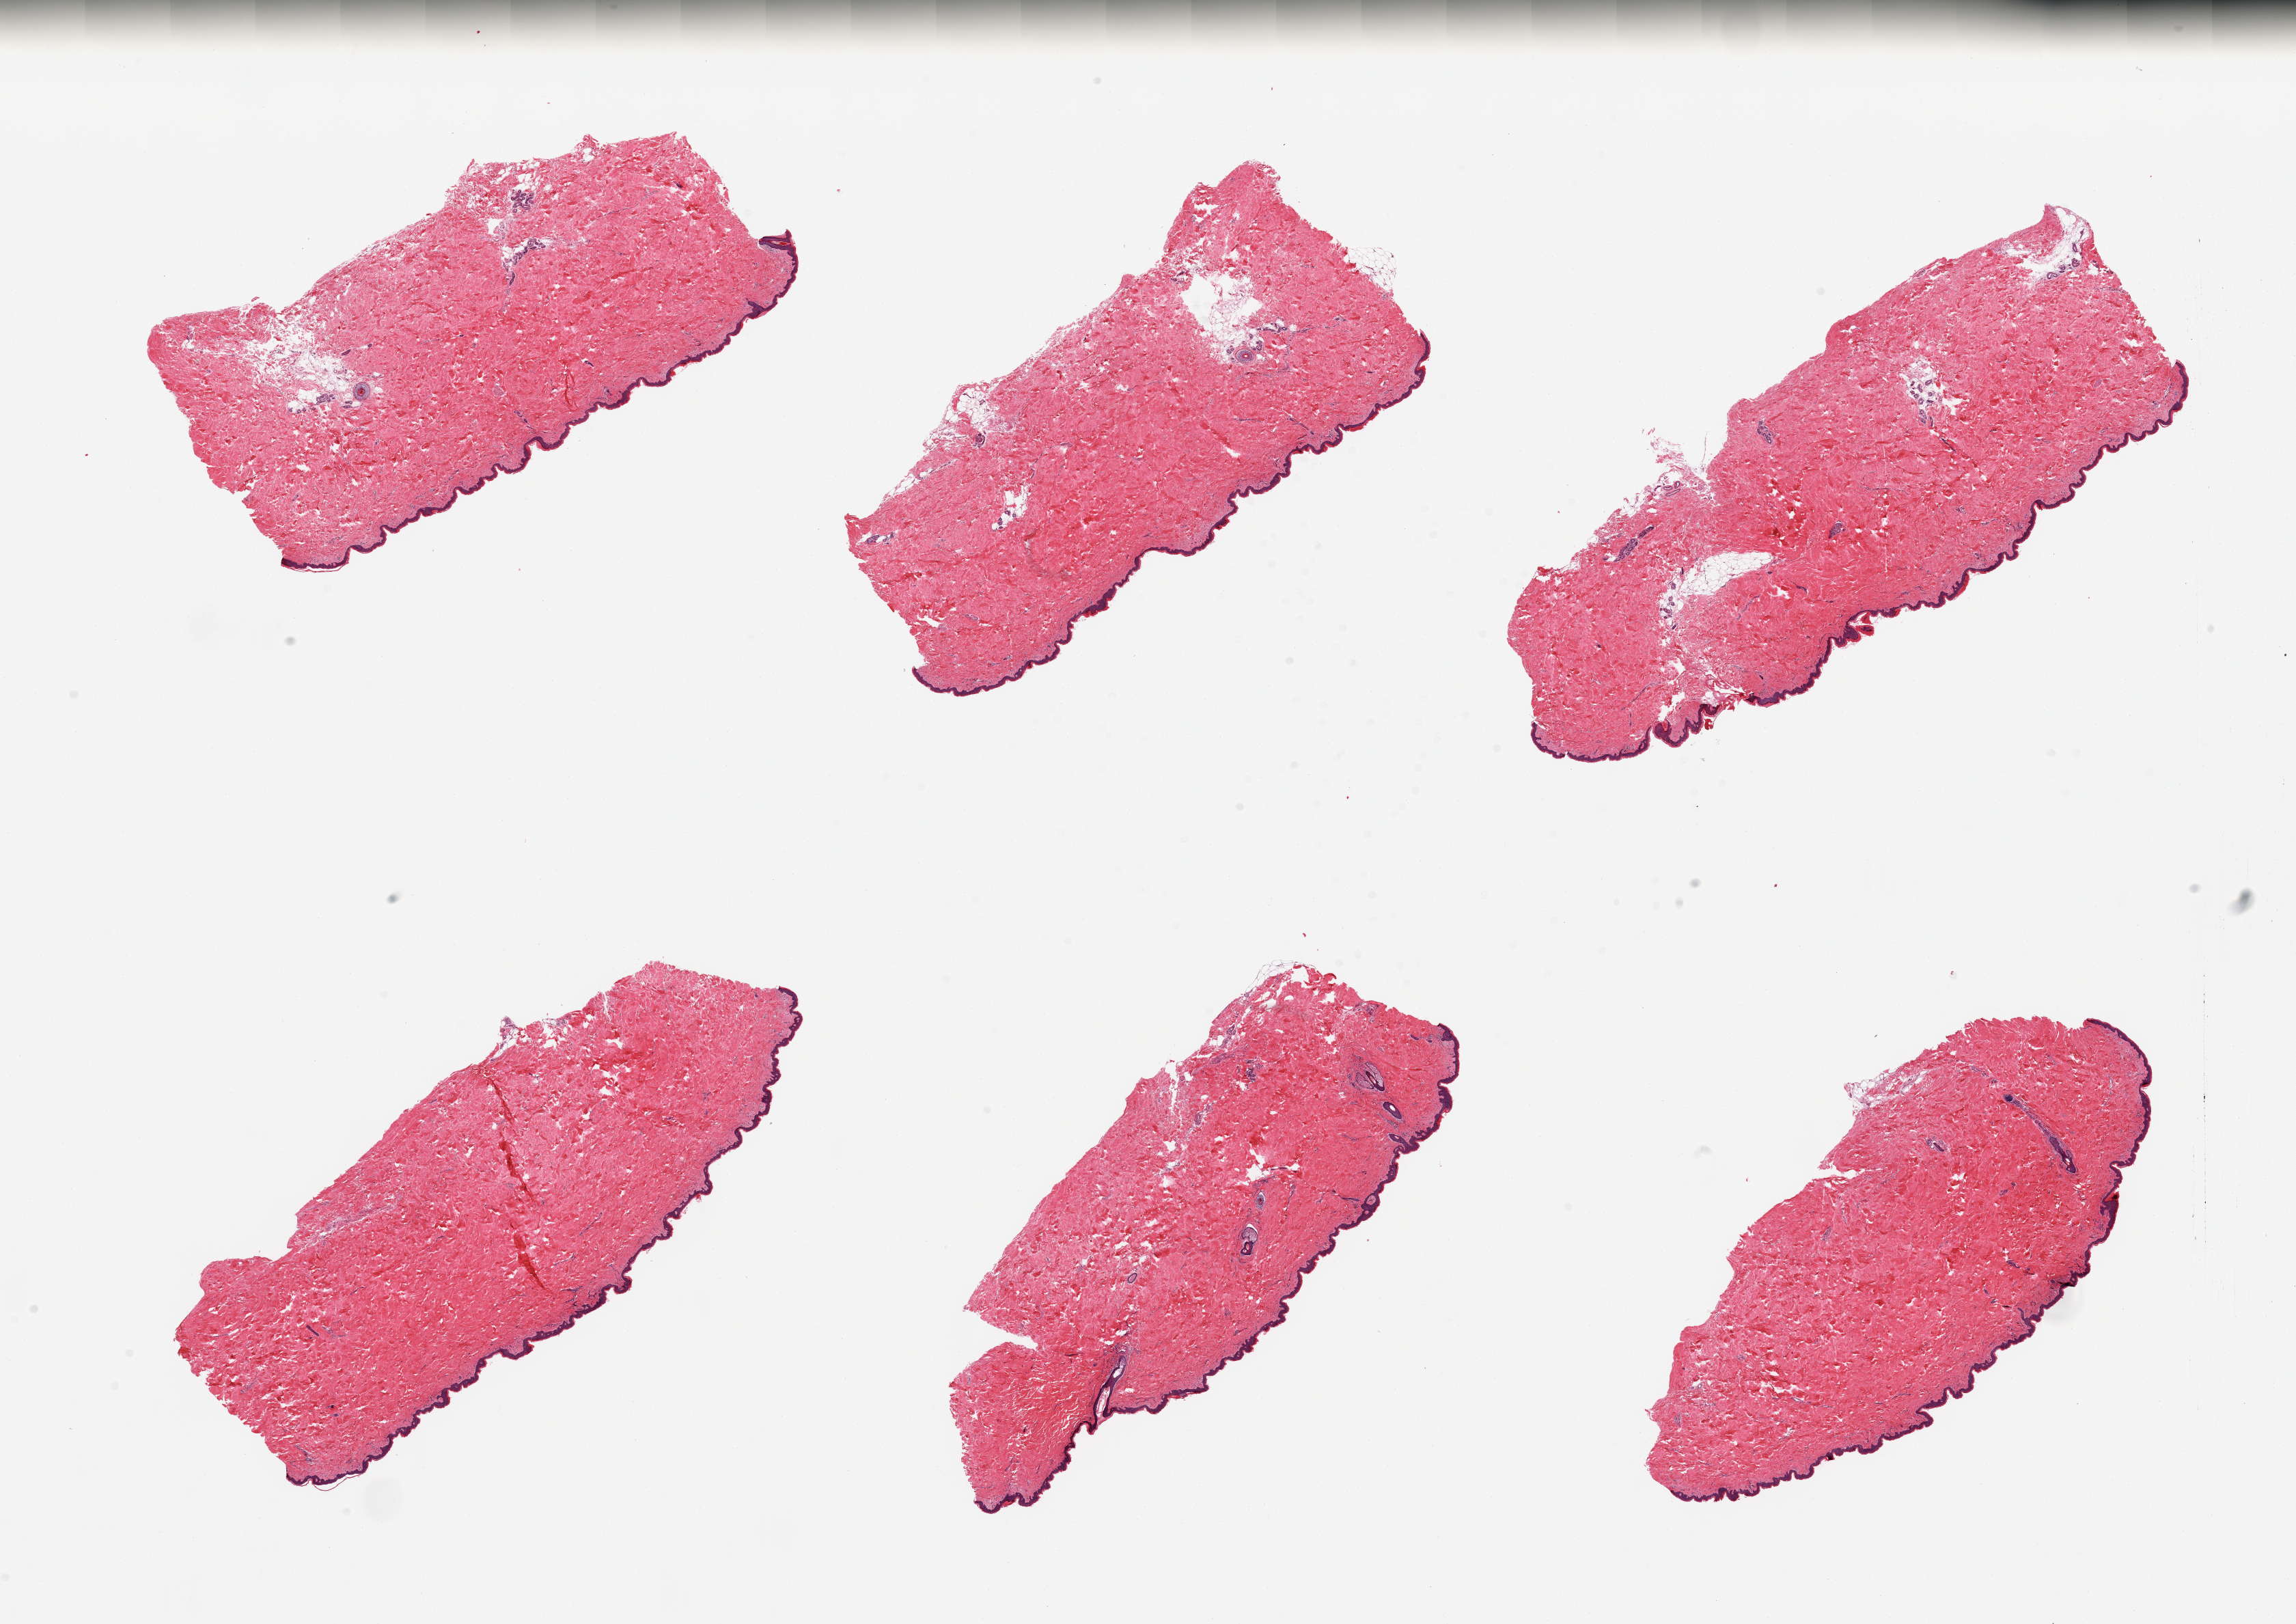
Whole-slide image, haematoxylin and eosin stain — whole scanned area (about 26.6 x 18.8 mm) shown as a low-resolution overview, PAXgene-fixed paraffin-embedded (PFPE) section, target tissue: skin of suprapubic region, donor tissue sample. Female donor.
- review note (as recorded): 6 pieces; well trimmed; up too 10% dermal fat